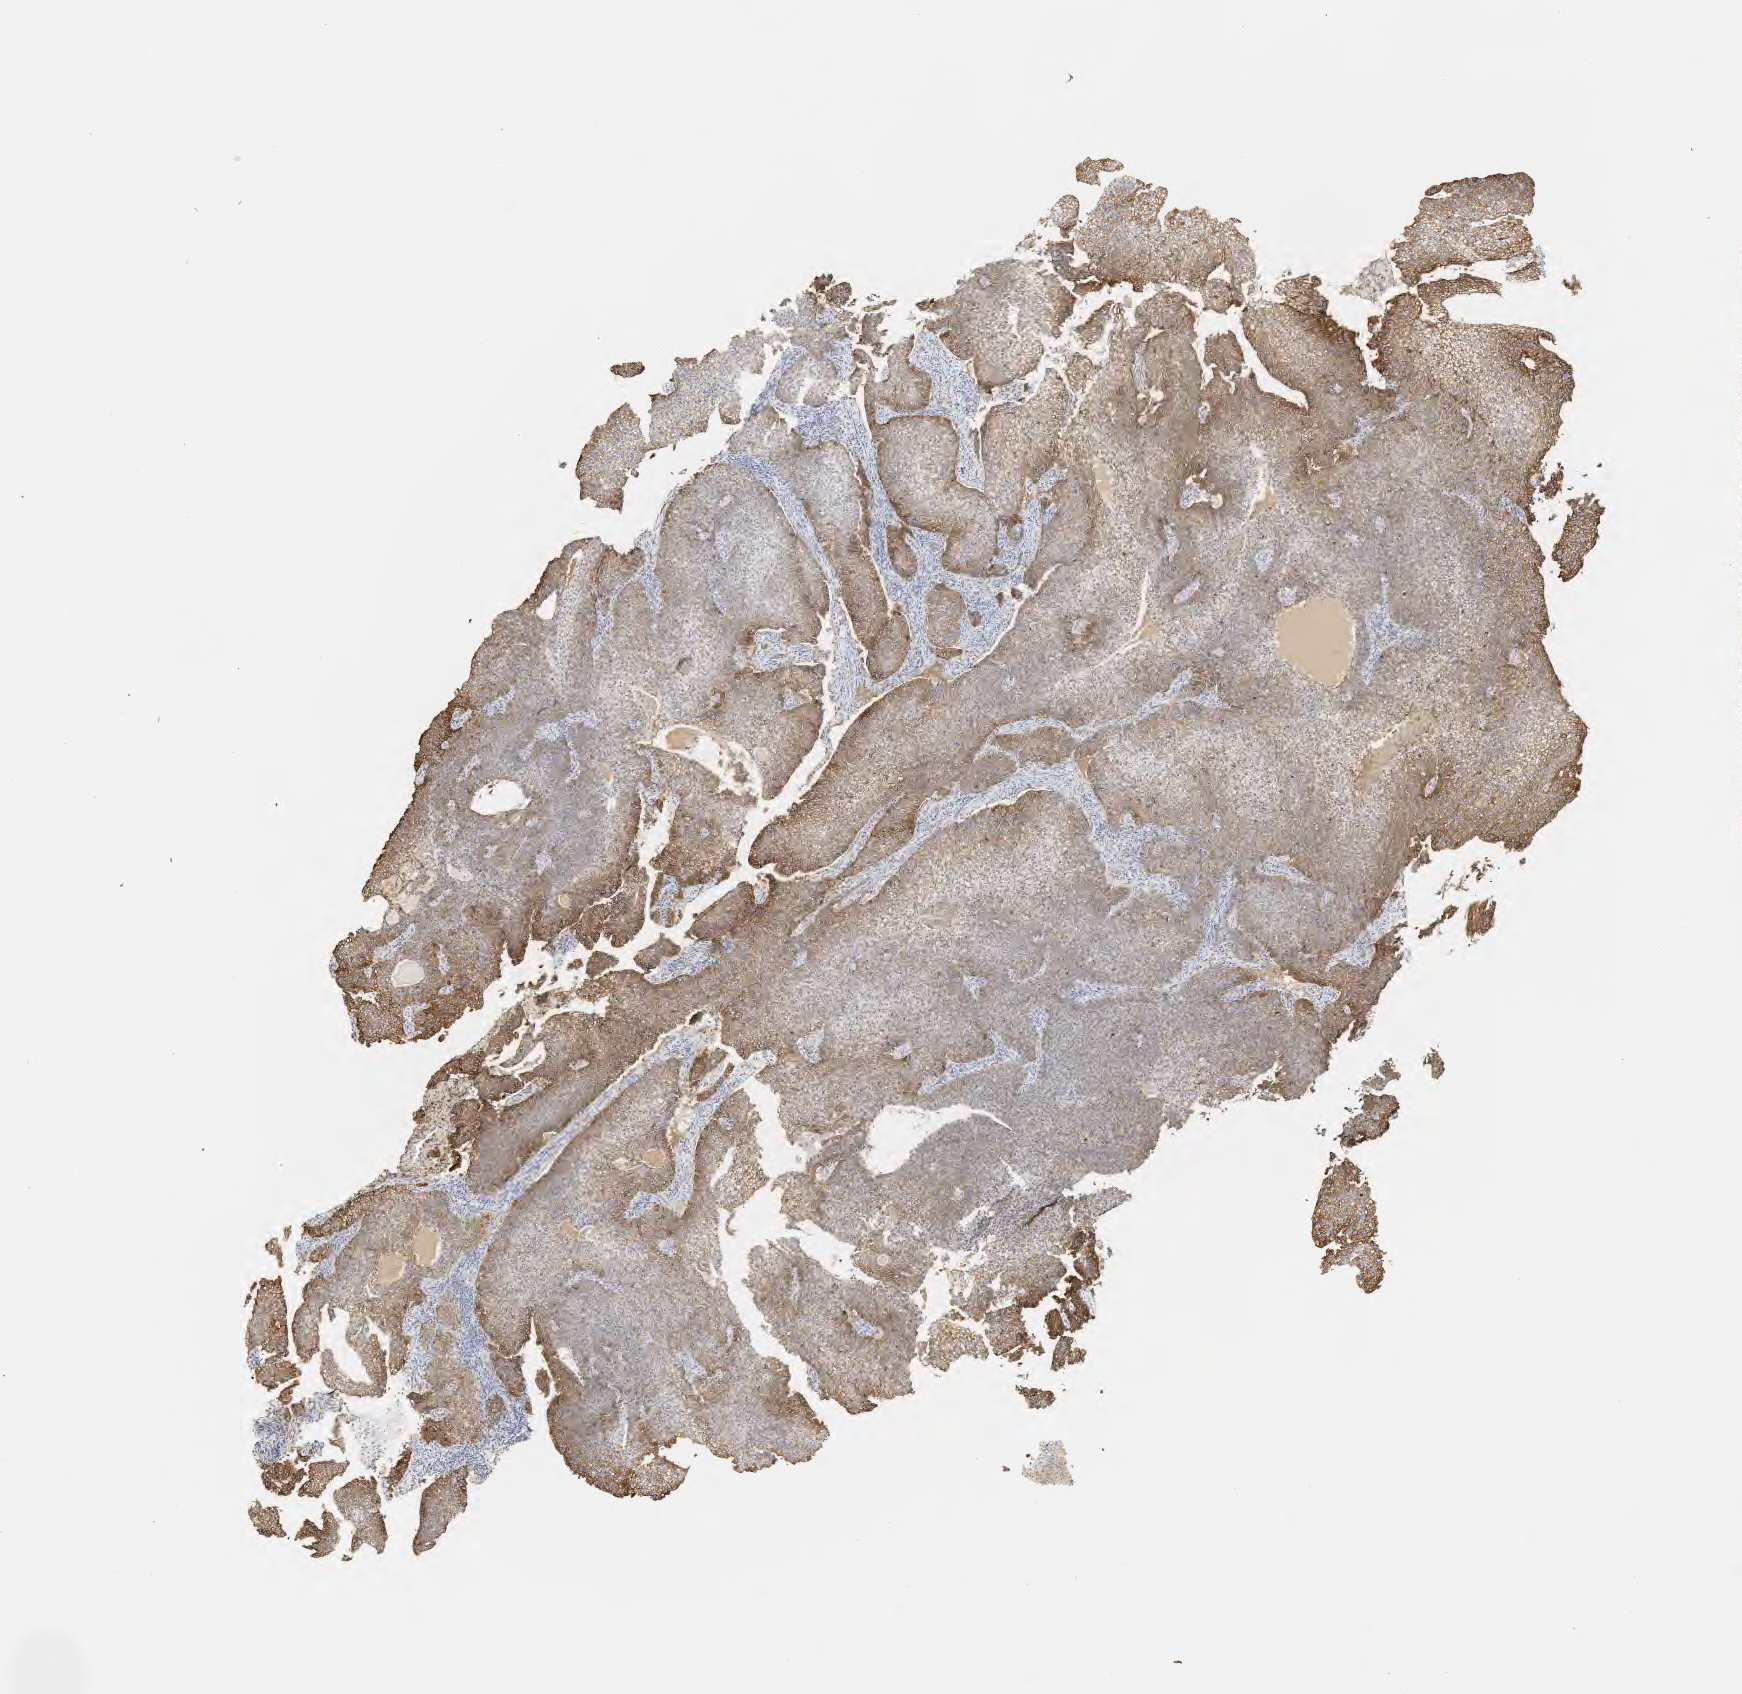
Whole-slide image, immunohistochemical stain for Ber-EP4, low-resolution overview of the scanned area, about 7.0 x 6.9 mm. Tumor tissue. Anatomic site: cervix. Patient: female, 39 years old.
Diagnosis: Squamous cell carcinoma, large cell, nonkeratinizing, NOS.